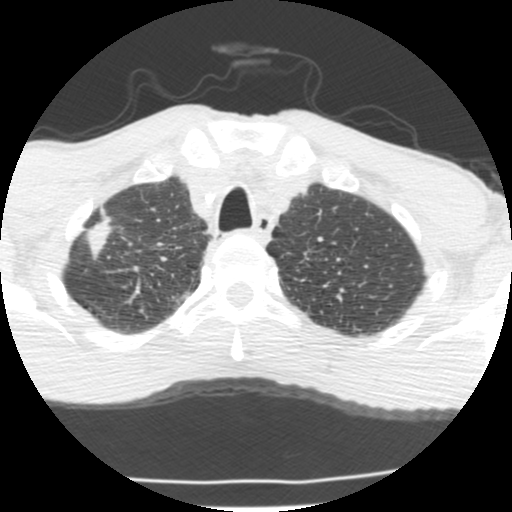
Chest CT (low-dose screening protocol), one axial image, second screening round (one year after baseline), lung window (W 1500 / L -600 HU), 2.5 mm slice thickness, standard (soft-tissue) reconstruction kernel (STANDARD). Male participant, aged 62 years at enrolment.
Lesion marked by an expert reader, bounding box [x1, y1, x2, y2] px = [61, 214, 134, 272]. The exam's reader record, not a measurement of the box and not confirmed to be the same lesion: non-calcified nodule or mass ≥4 mm, right upper lobe, 23 × 11 mm, spiculated (stellate) margins, soft tissue attenuation, pre-existing on the prior screen: yes. Participant outcome: lung cancer diagnosed 277 days after this screen — adenocarcinoma, NOS, right upper lobe, poorly differentiated (G3), stage IIA (AJCC 6th edition), 22 mm at pathology.